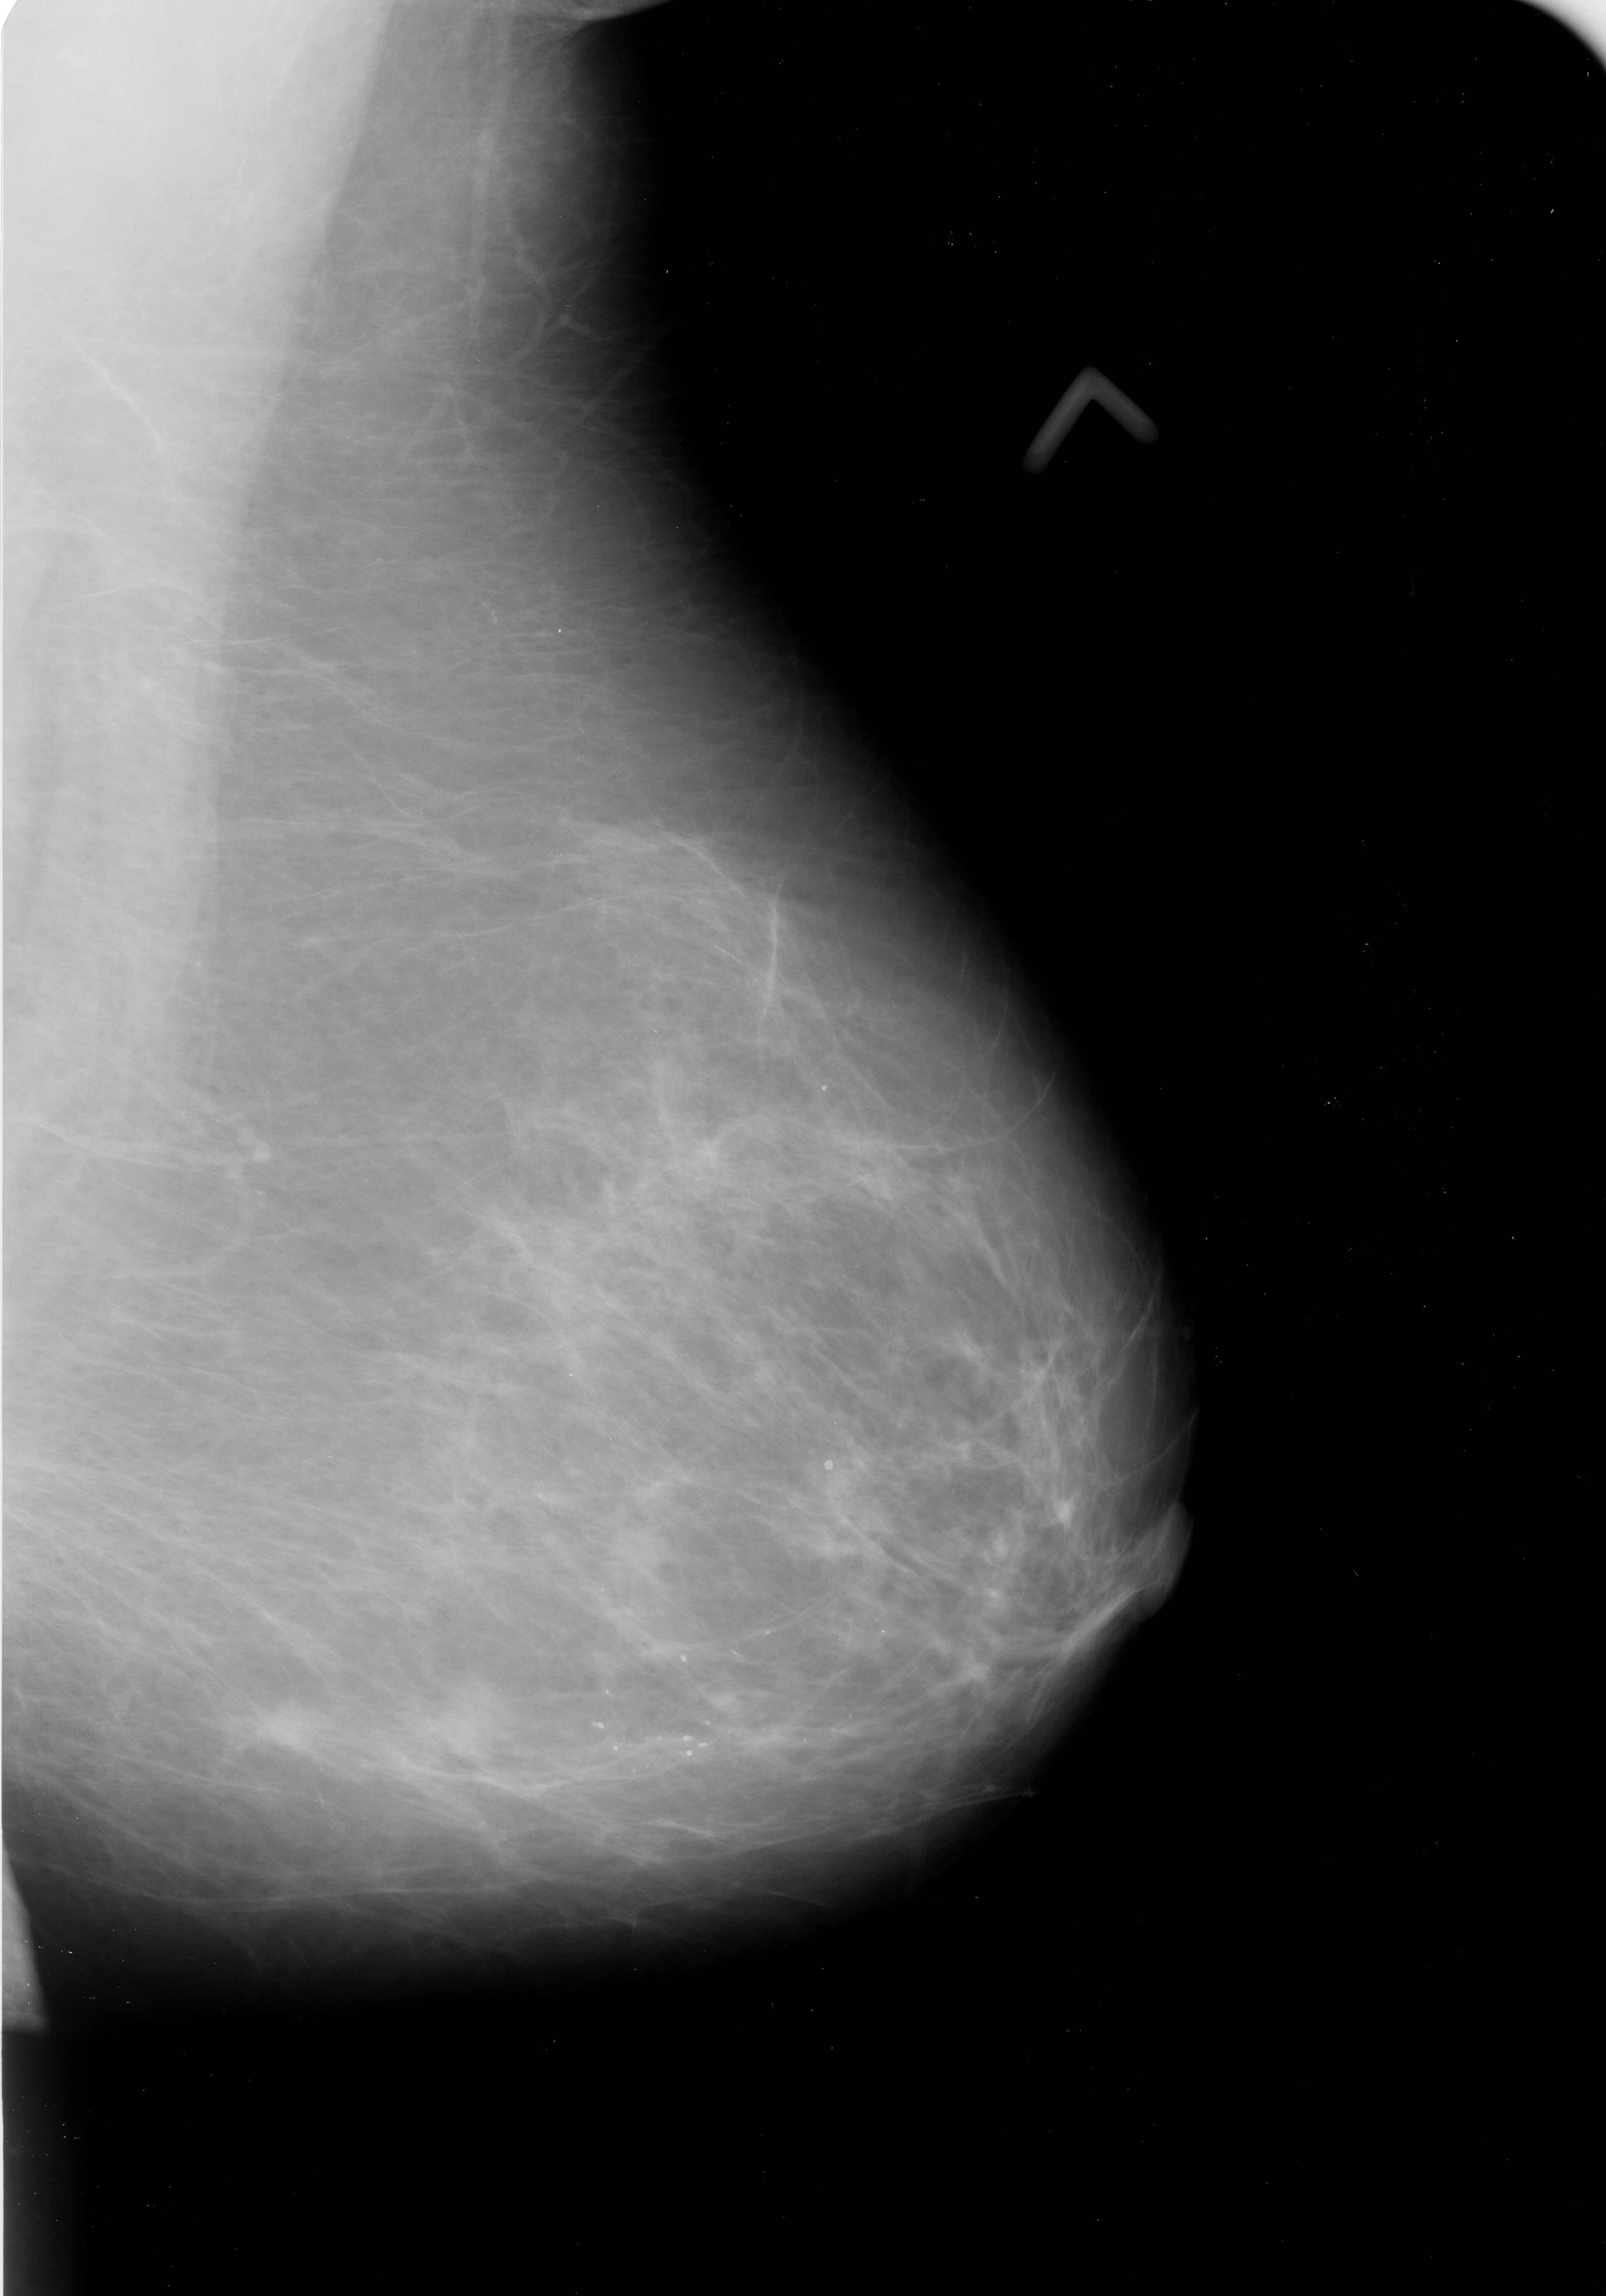
Mammogram (digitized film); left breast; mediolateral oblique (MLO) view; 1606 × 2296 image matrix.
Marked abnormalities (boxes around the expert regions of interest):
- Finding 1 of 2: mass, shape irregular, margins spiculated; BI-RADS assessment category 4; subtlety rating 3 on a 1 (subtle) to 5 (obvious) scale; pathology result (as recorded, not read from the image): malignant: bounding box (x1, y1, x2, y2) in pixels: (418, 1672, 514, 1770)
- Finding 2 of 2: mass, shape irregular, margins spiculated; BI-RADS assessment category 4; subtlety rating 3 on a 1 (subtle) to 5 (obvious) scale; pathology result (as recorded, not read from the image): malignant: (609, 1524, 684, 1593)